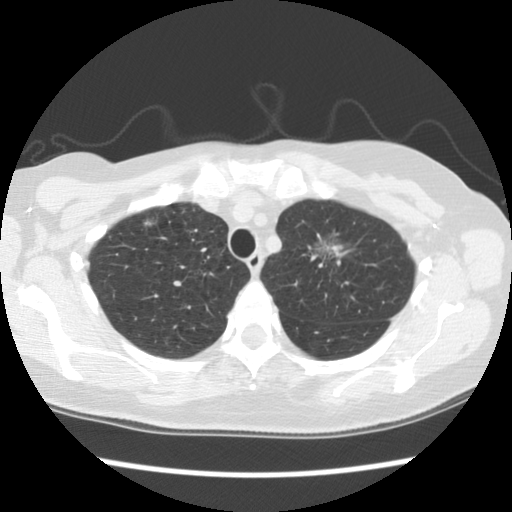
Chest CT (low-dose screening protocol), one axial image, second annual screen, lung window (W 1500 / L -600 HU). Female participant, aged 65 years at enrolment. Former smoker at enrolment.
Expert reader's lesion annotation, bounding box <300,224,364,284> (left, top, right, bottom; pixels). The screening reader recorded 2 non-calcified nodules or masses ≥4 mm on this exam (right upper lobe, left upper lobe); which of them this box marks is not recorded. Lung cancer was diagnosed 481 days after this screen: adenocarcinoma, NOS, left upper lobe, moderately differentiated (G2), stage IA (AJCC 6th edition), 30 mm at pathology.